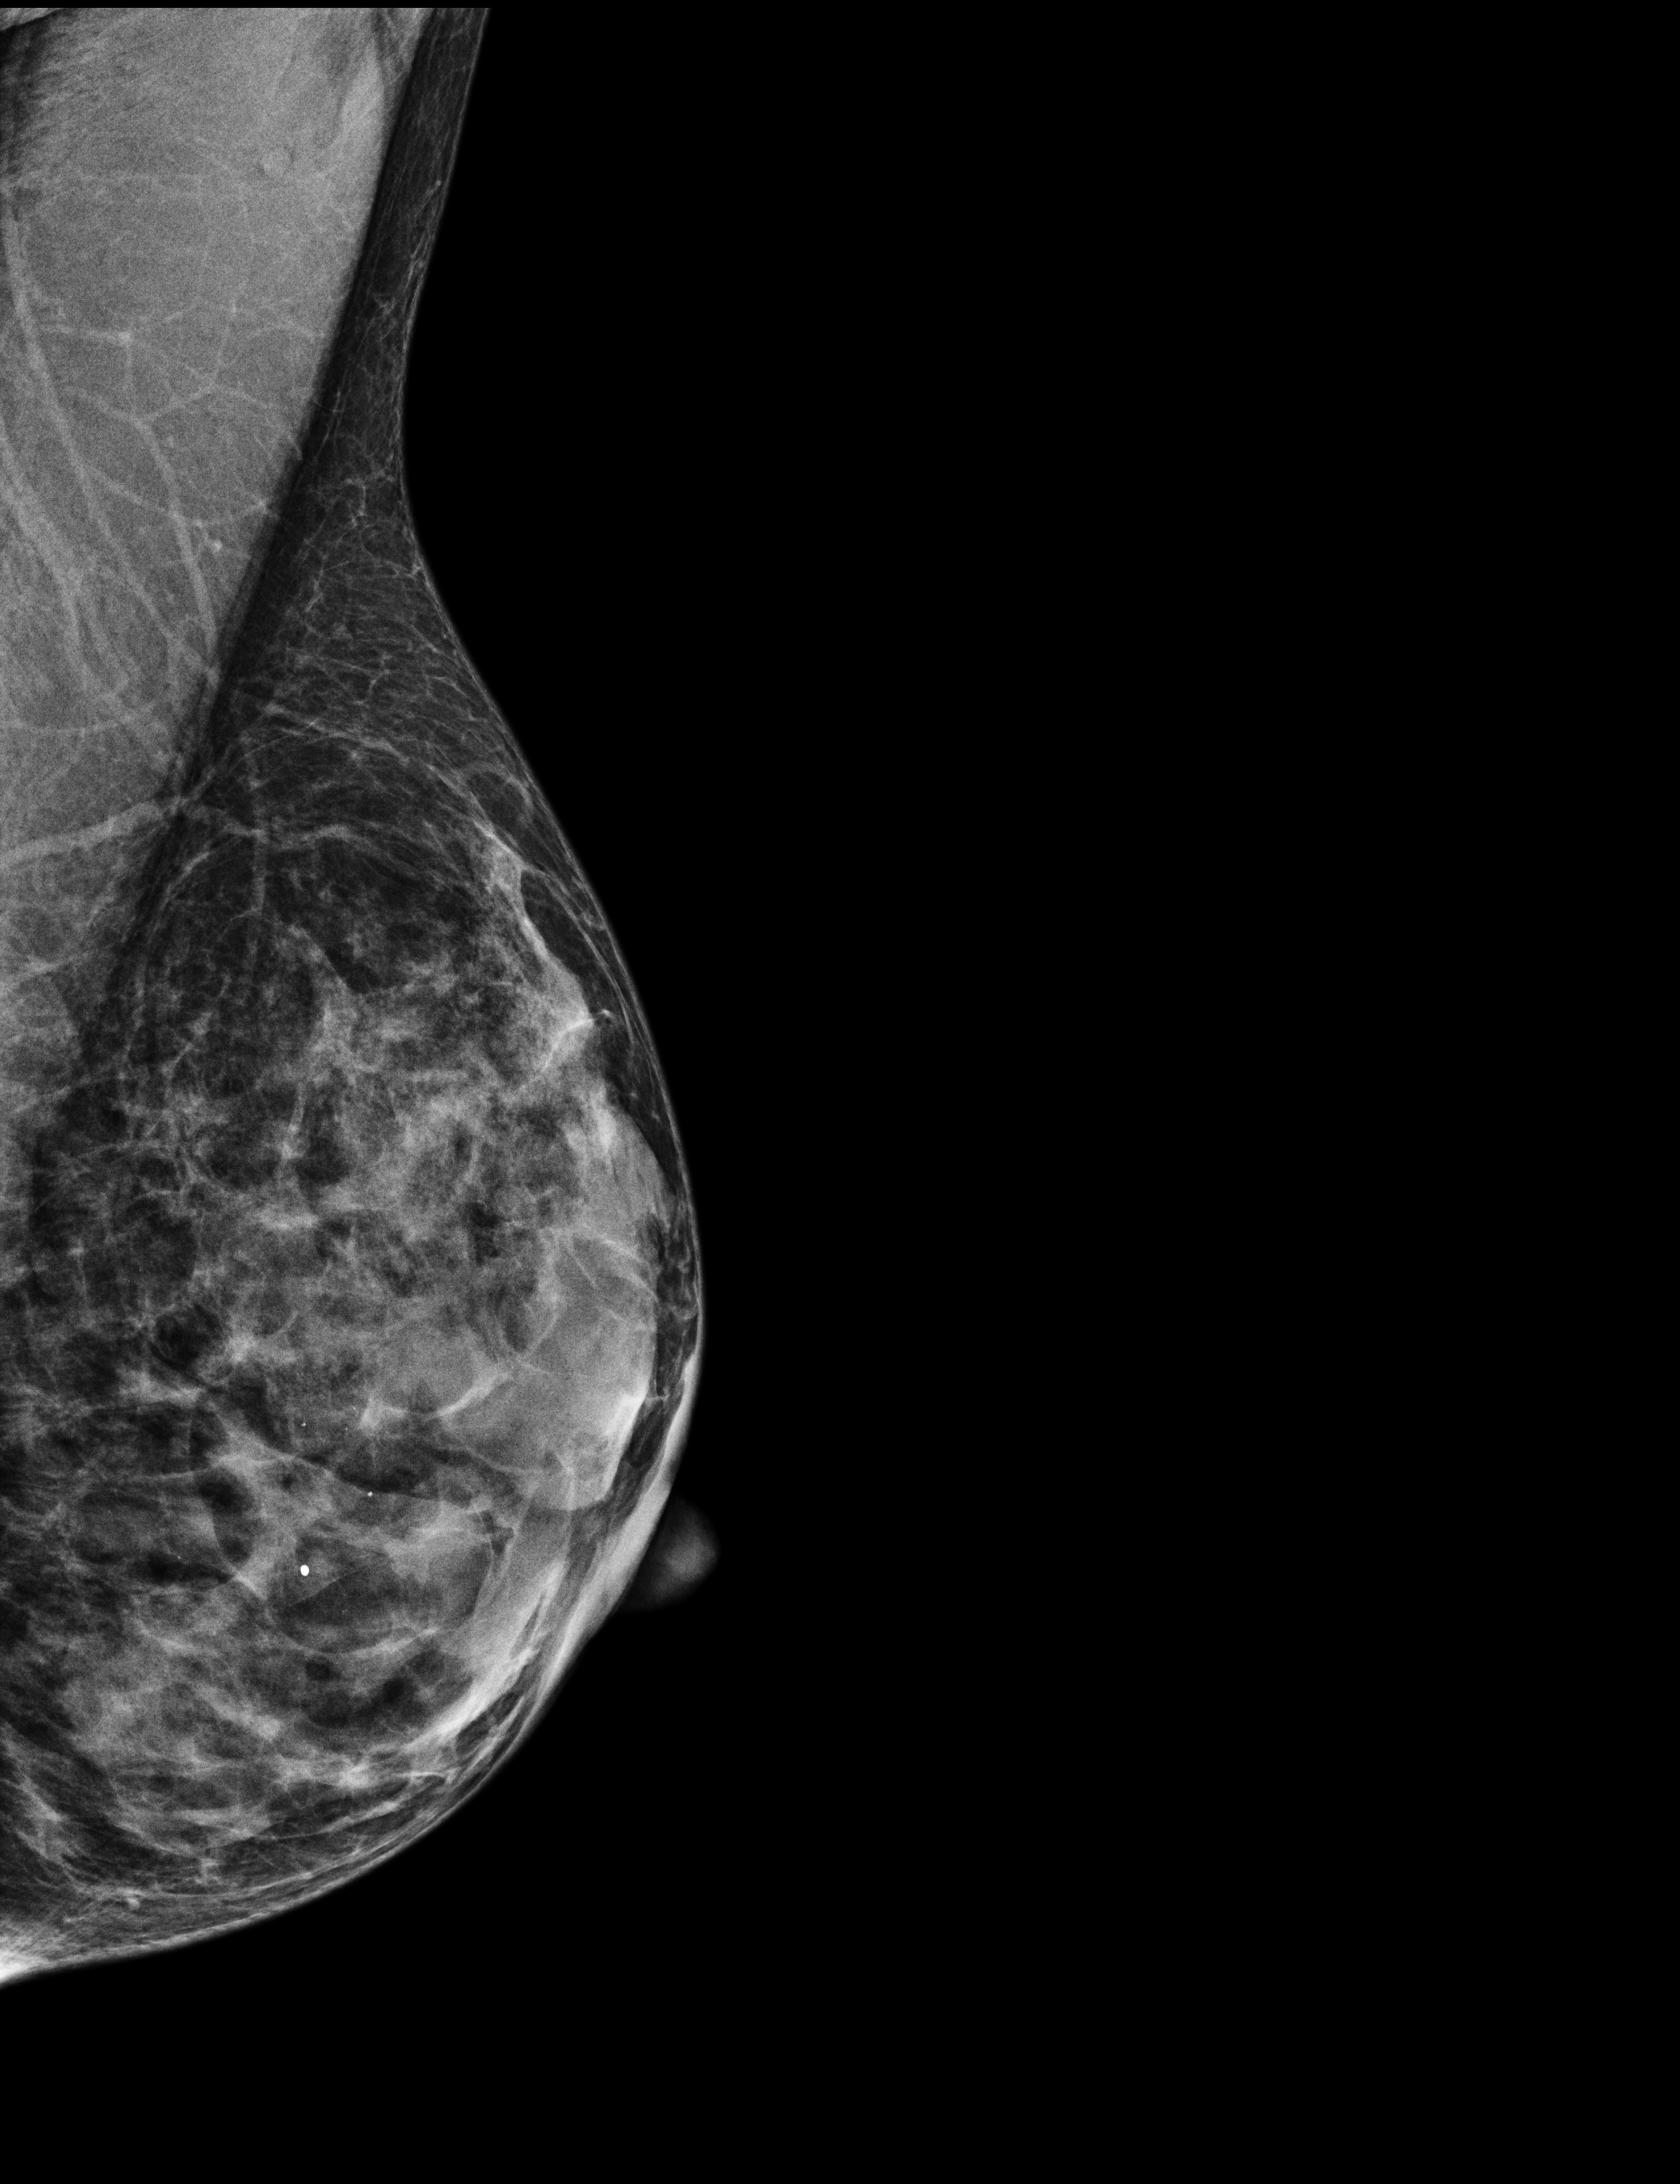
Screening examination; system: Selenia Dimensions. Female patient, age 59 years.
Image type: full-field digital mammogram. Breast: left. Projection: MLO view.